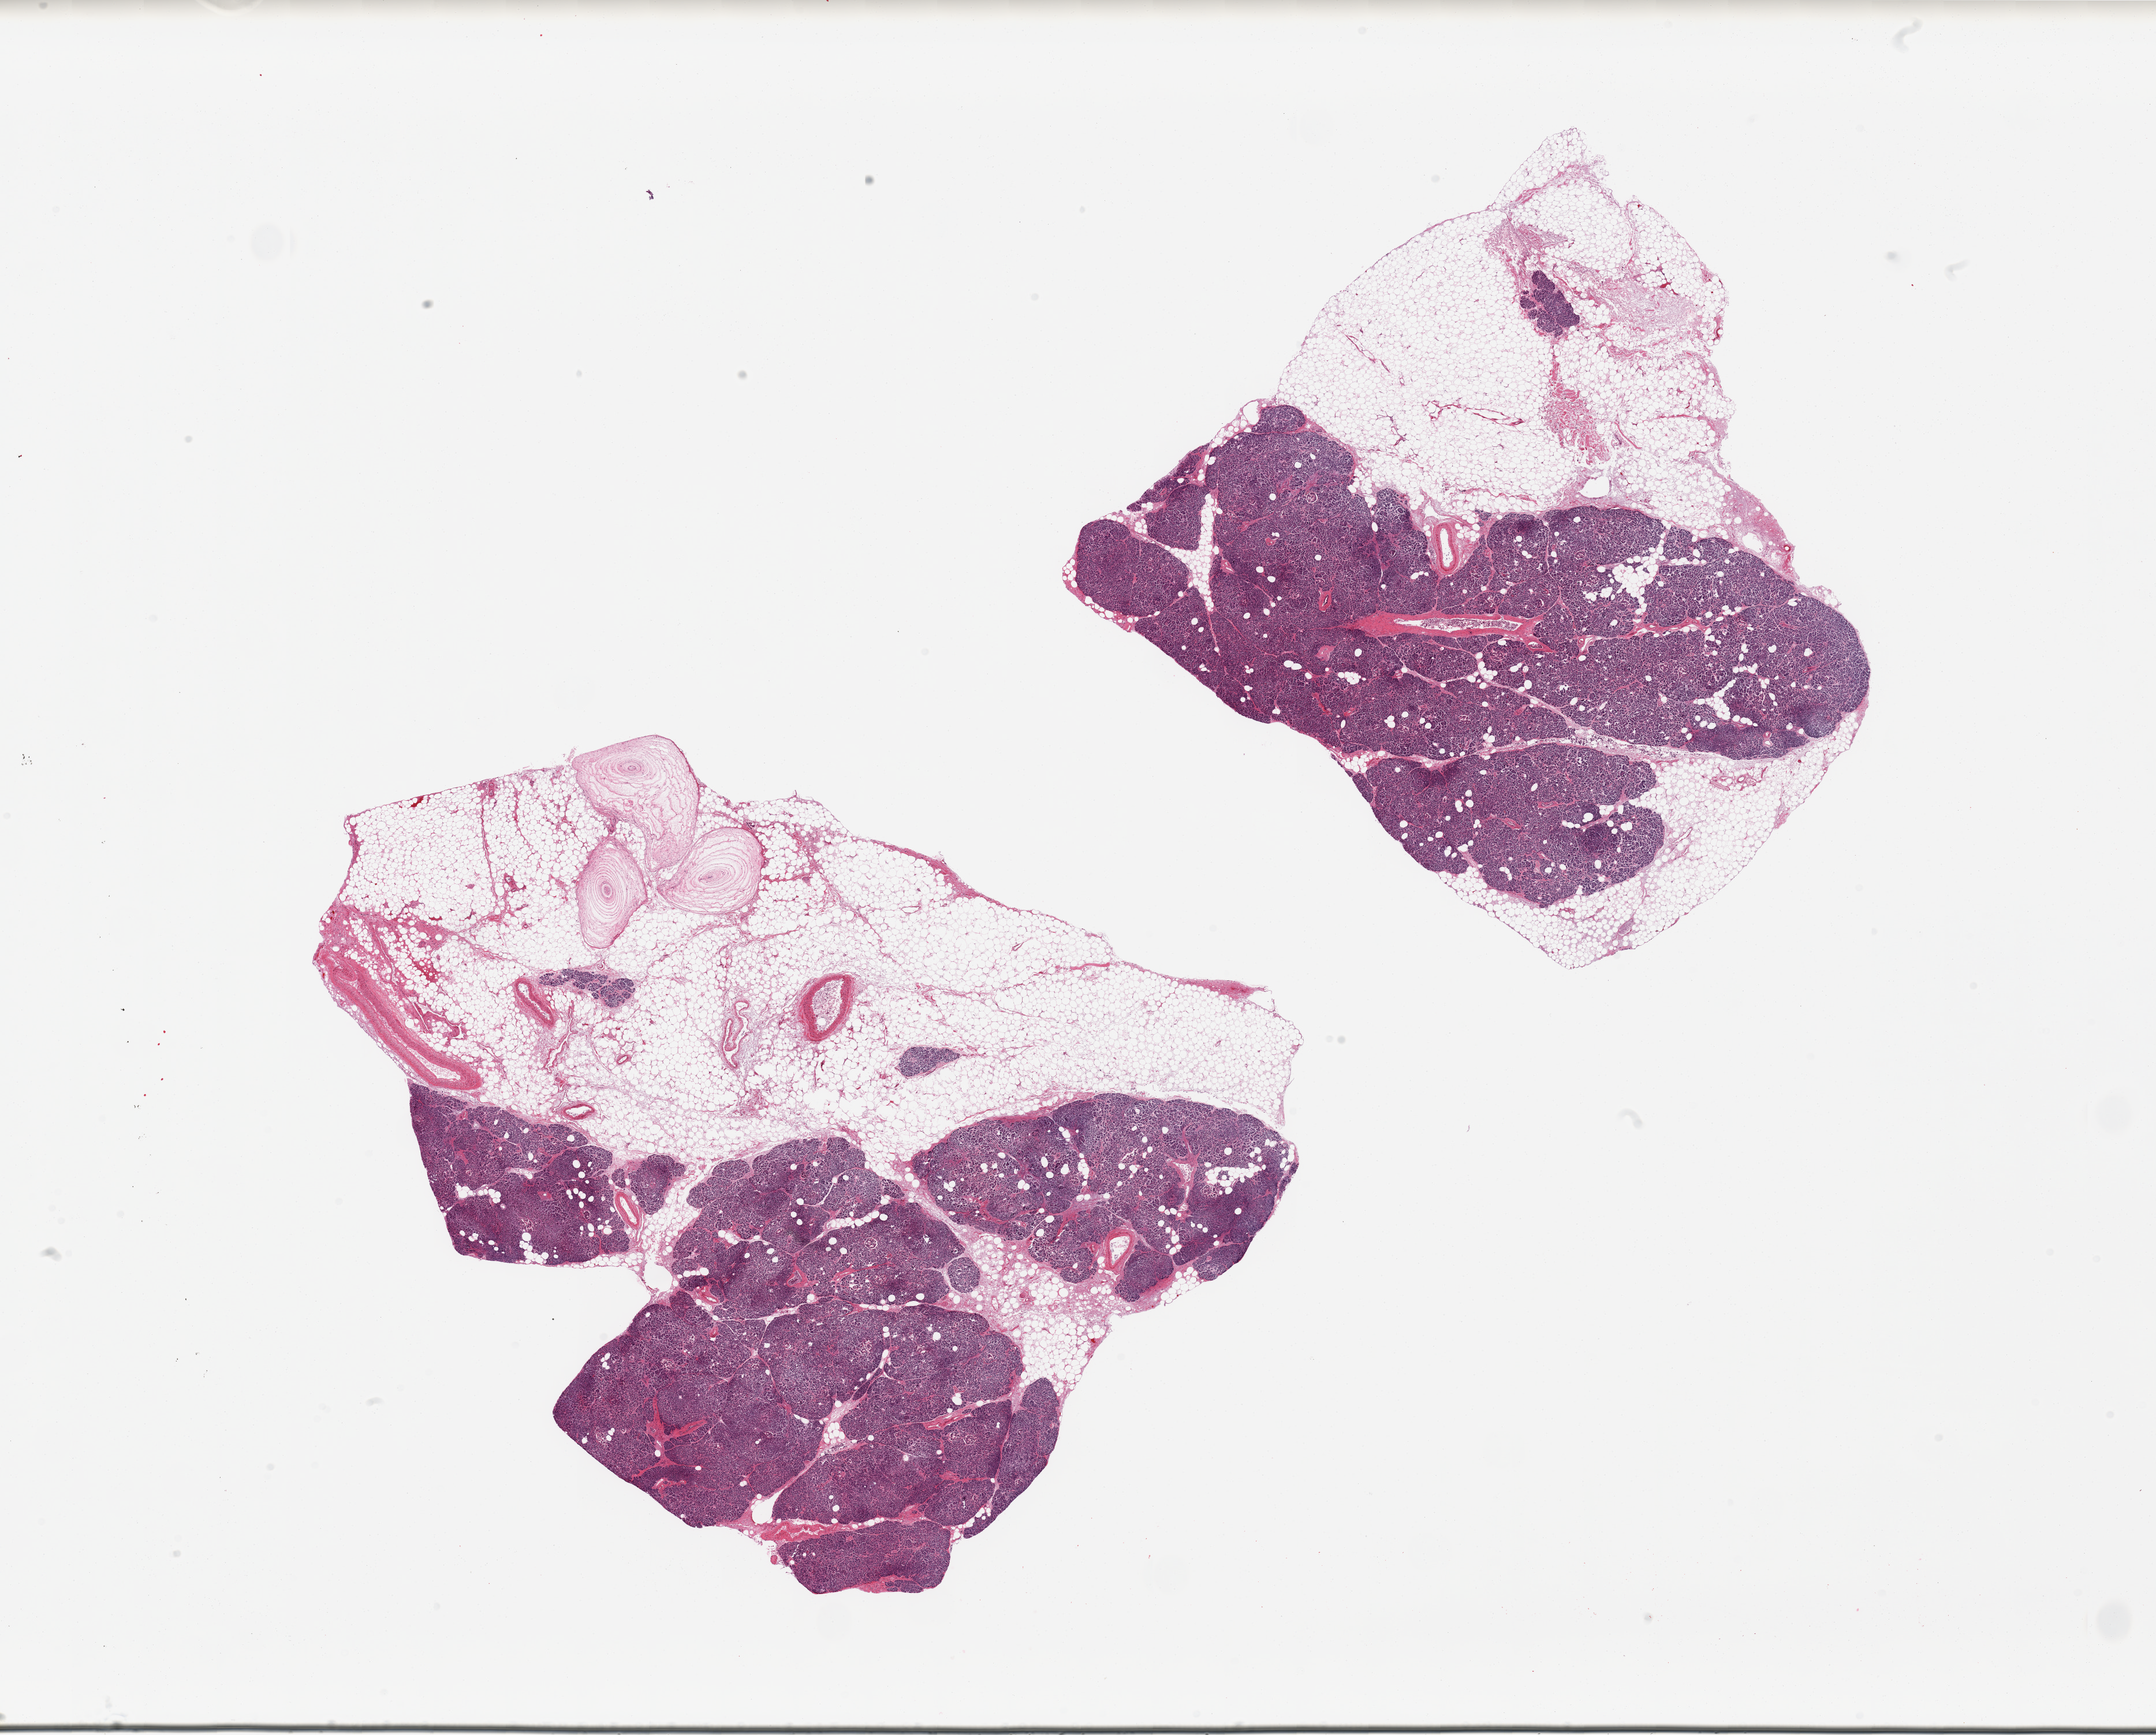
Whole-slide image, hematoxylin and eosin (H&E) stain, brightfield, shown as a low-resolution overview of the whole scanned area (about 29.5 x 23.8 mm); PAXgene-fixed paraffin-embedded (PFPE) section; sampled site (target tissue): pancreas; donor tissue sample. Donor sex: male.
* review note (as recorded): 2 pieces, ~50% fat, moderate saponification, Islets not well seen